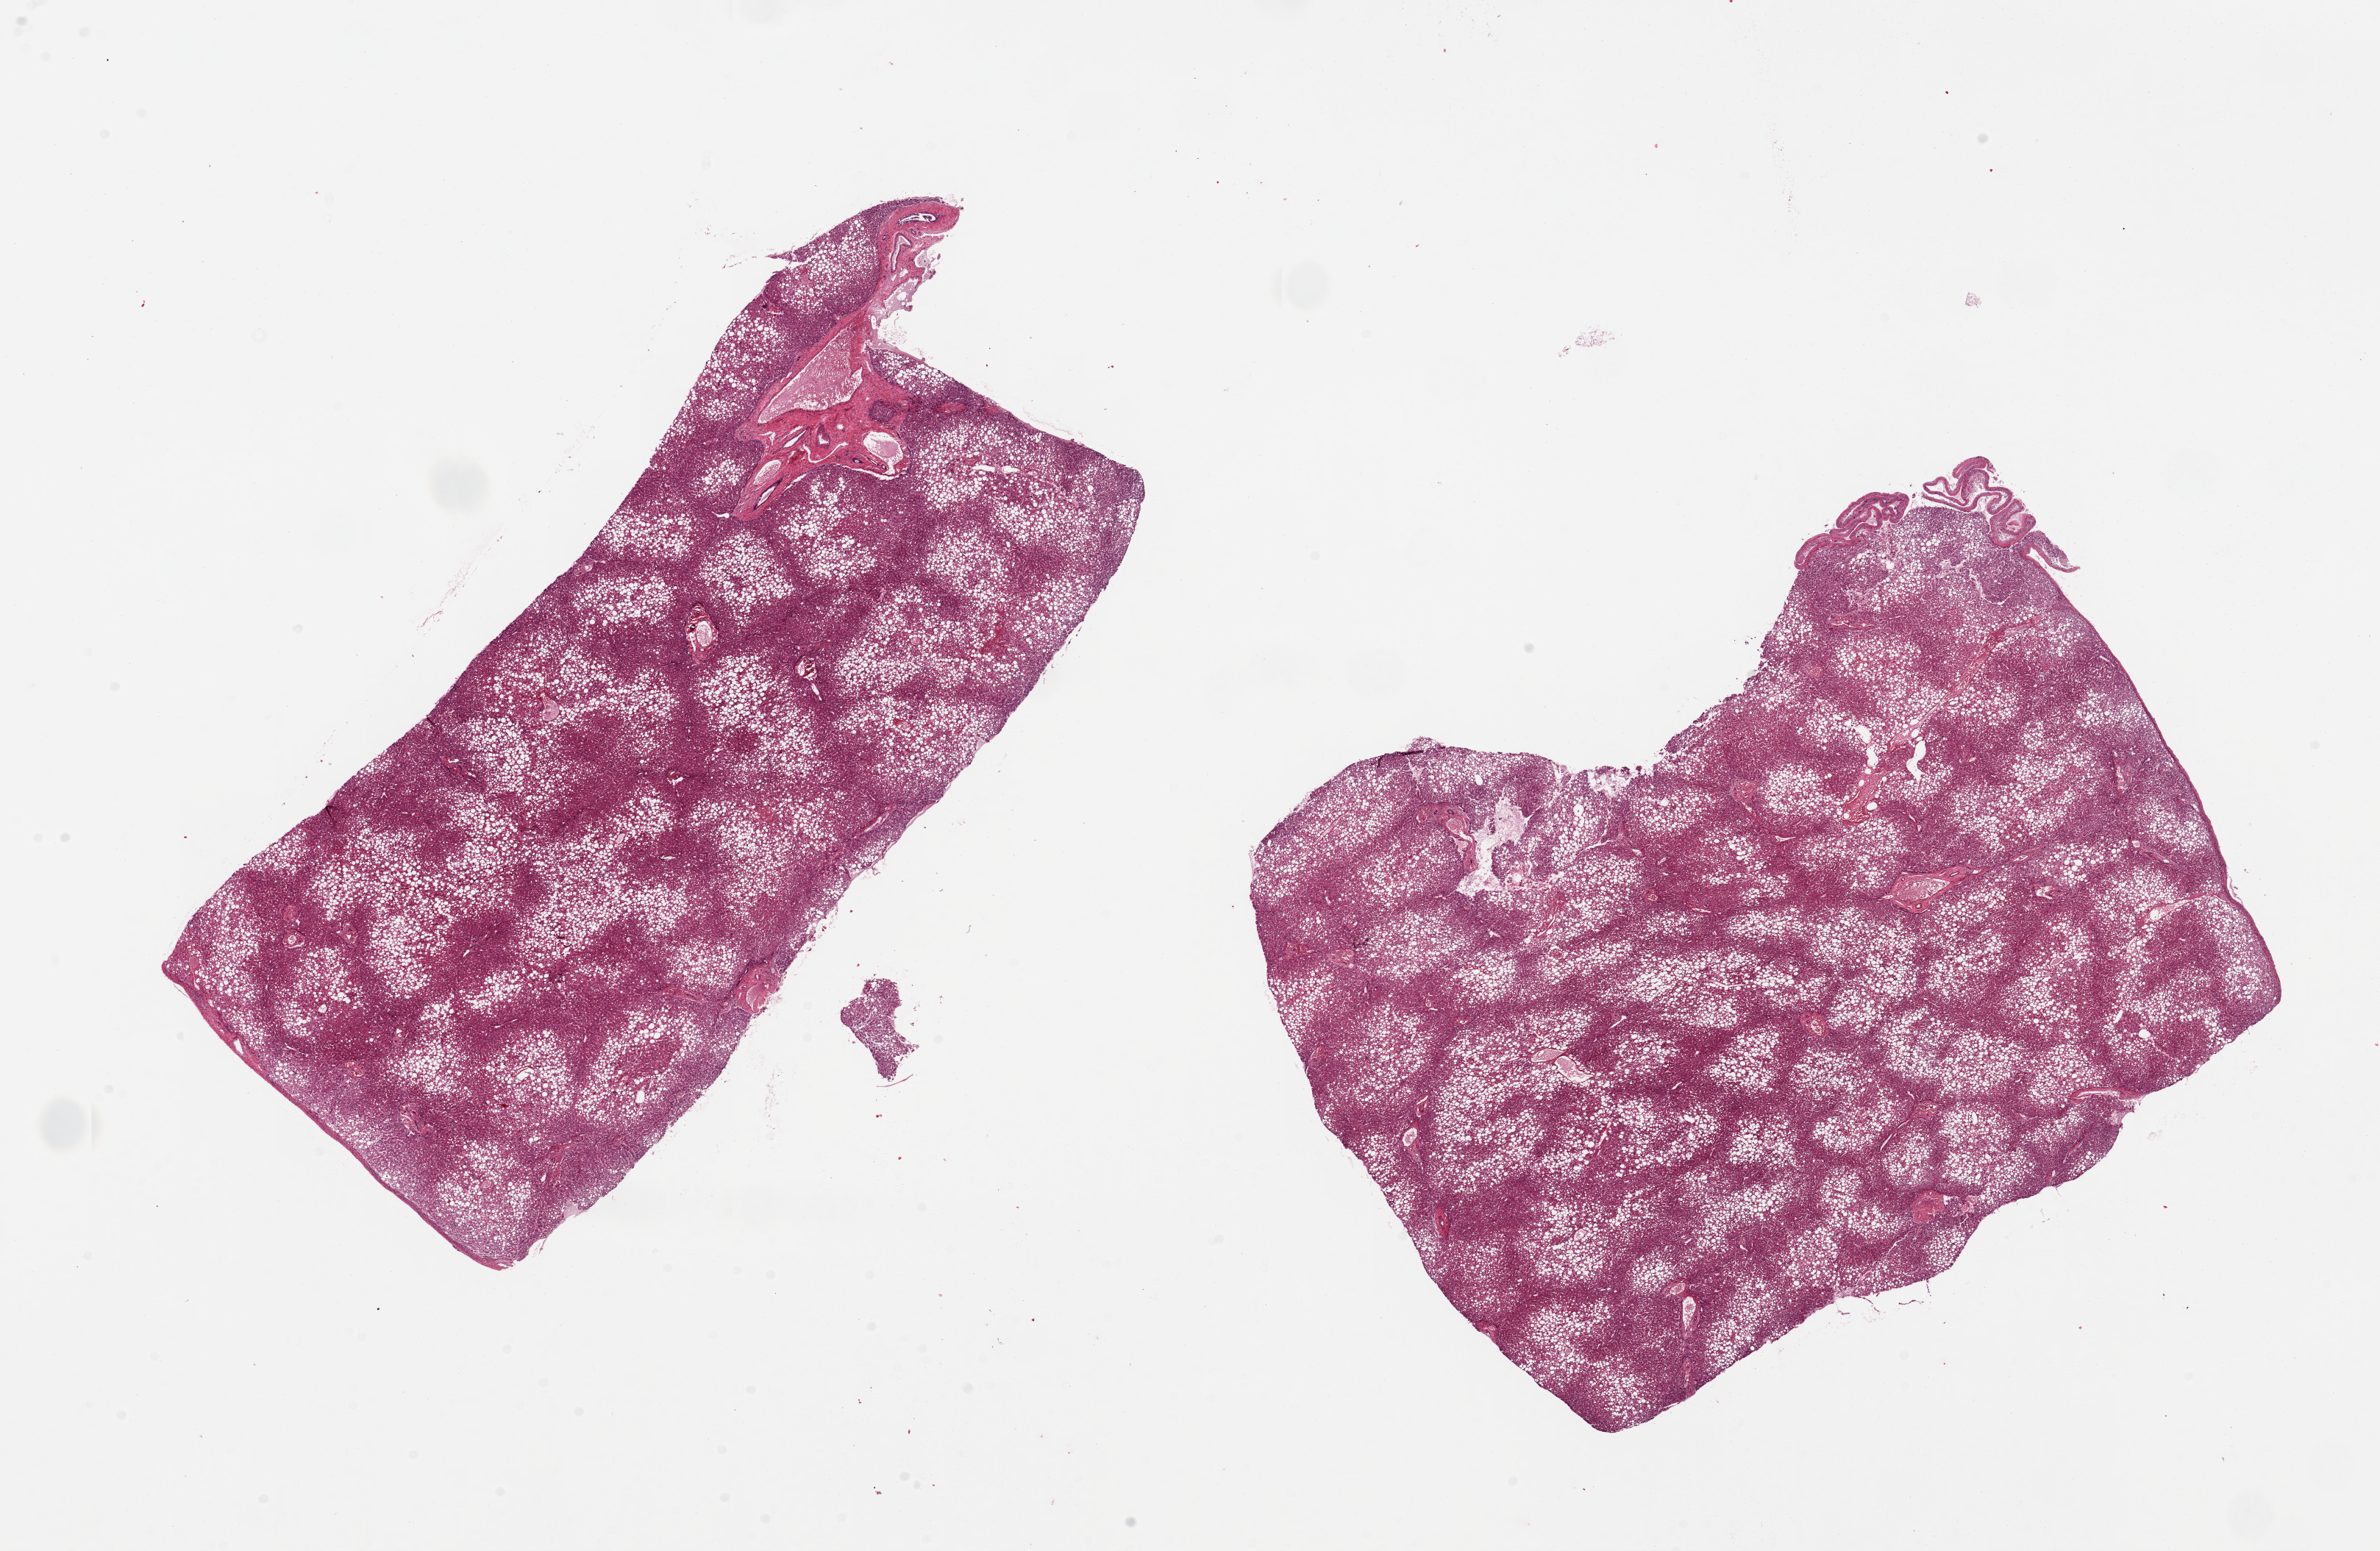
Whole-slide image, haematoxylin and eosin stain, brightfield, a low-resolution overview of the entire scanned area, about 25.6 x 16.7 mm. PAXgene-fixed paraffin-embedded (PFPE) section. Sampled site (target tissue): liver. Tissue donor sample. Male donor.
Reviewer comment on this tissue sample: 2 pieces, 12x5 and 10x8mm; diffuse macrovesciular steatosis involves ~80% of parenchyma.